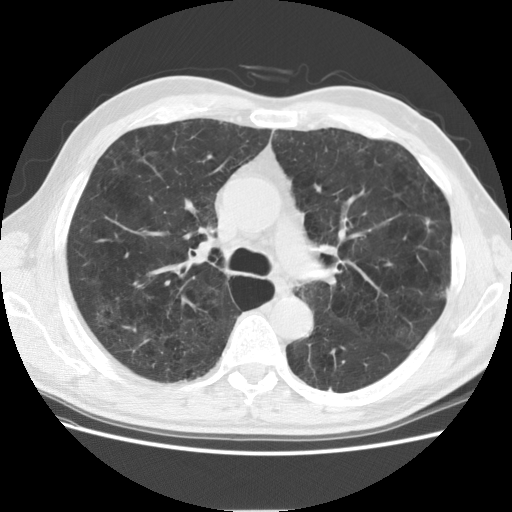
Chest CT (low-dose screening protocol), one axial image. Second screening round (one year after baseline). Lung window (W 1500 / L -600 HU). 2.5 mm slice thickness. Standard (soft-tissue) reconstruction kernel (STANDARD). 120 kVp. Slice 69 of 180 in the series. 512 × 512 image matrix. Male participant, aged 58 years at enrolment. Current smoker at enrolment.
Expert-annotated lung lesion, bounding box [x1, y1, x2, y2] px = [413, 209, 445, 242]. Screening reader's record for this exam: no non-calcified nodule ≥4 mm recorded. Participant outcome: lung cancer diagnosed 389 days after this screen (after the third annual screen) — adenocarcinoma, NOS, left upper lobe, stage IA (AJCC 6th edition), 9 mm at pathology.